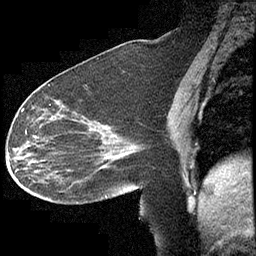
Breast MRI (dynamic contrast-enhanced), one sagittal slice. Position 165 of 232 along the scan axis. Dynamic contrast-enhanced study with each time point stored as its own series, time point 2 of 4 at this slice position (early post-contrast, ordered by acquisition time). 1.5 T. TE 4.2 ms, TR 6.7 ms. 3 mm slice thickness. 256 × 256 image matrix. Patient: female, 63 years. Case-level facts recorded for this patient, not image findings: setting: breast cancer imaged before/during neoadjuvant chemotherapy; receptor status: triple-negative.
Annotated regions visible in this slice (semi-automatically segmented with operator editing):
- analysis volume of interest (the breast-tissue region the enhancement analysis was run in; not a lesion): box from (x=13, y=90) to (x=140, y=205) px
- tumour enhancement mask (voxels above the 70 % enhancement threshold inside the analysis volume of interest): (x=22, y=108)–(x=30, y=154)